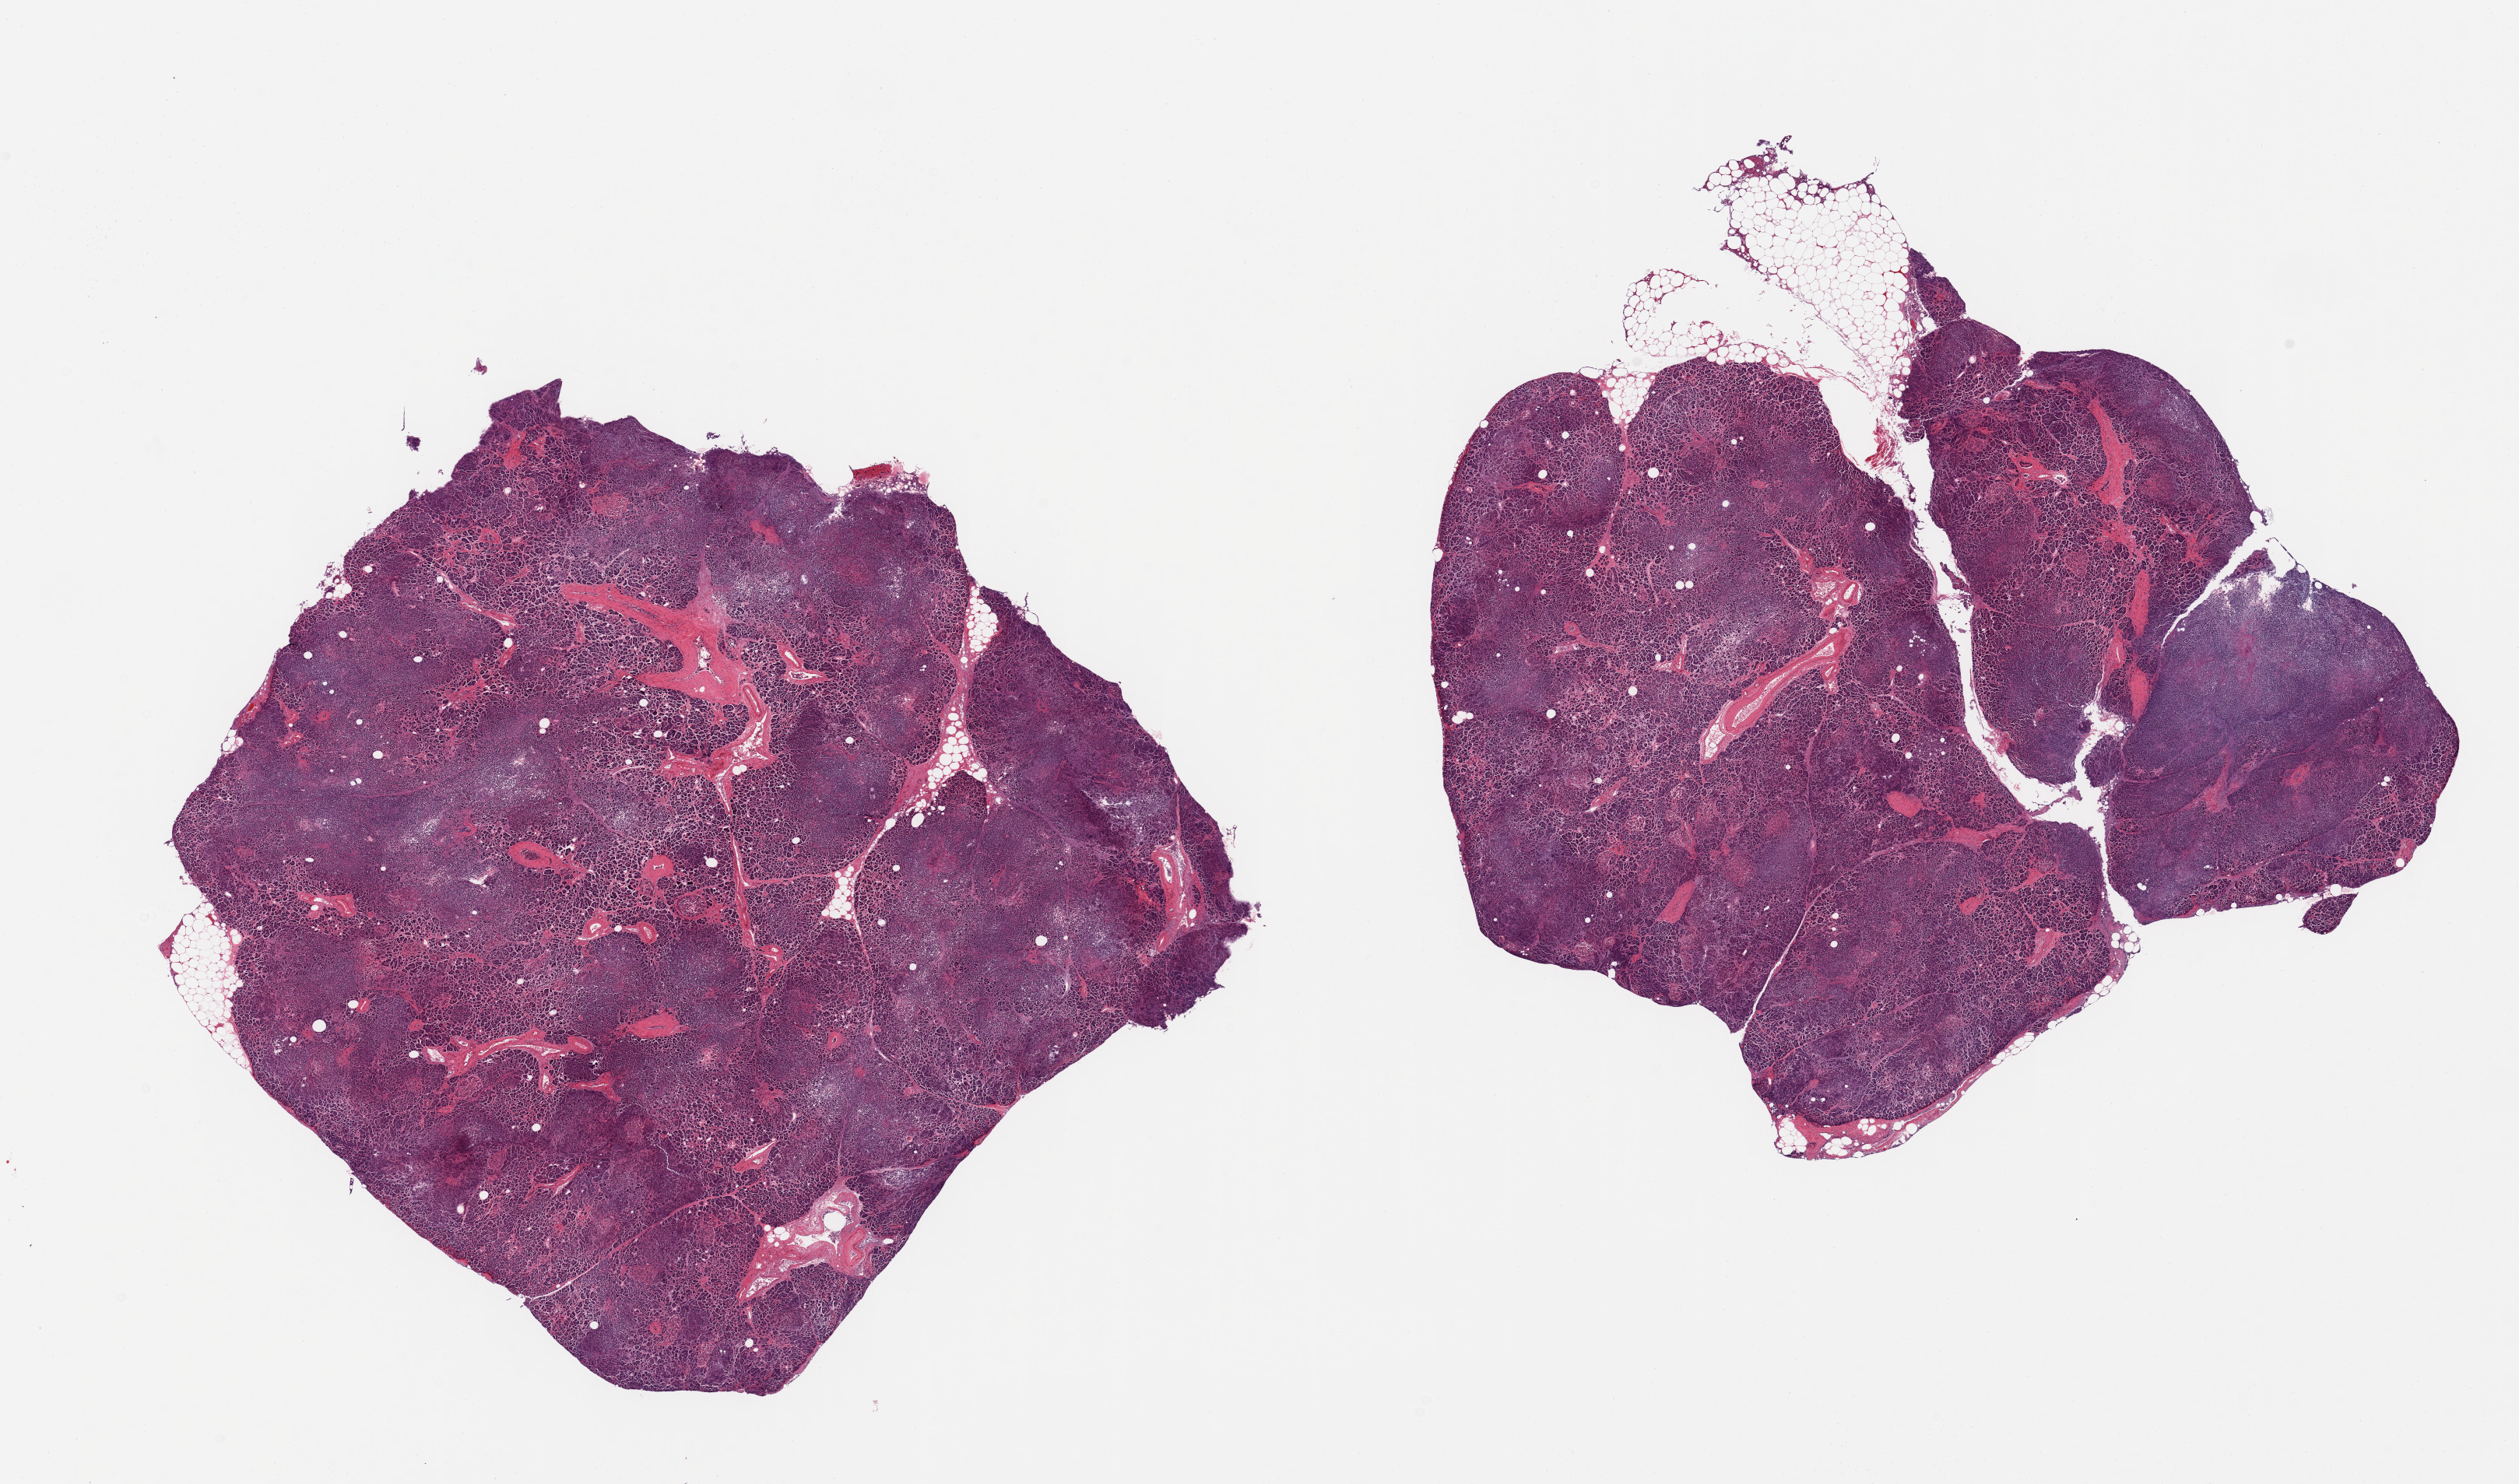
H&E whole-slide image, shown as a low-resolution overview of the whole scanned area (about 25.6 x 15.1 mm). PAXgene-fixed paraffin-embedded (PFPE) section. Sampled site (target tissue): pancreas. Donor tissue sample. Donor sex: male.
Pathologist's review note for this sample: 2 pieces; 1 includes ~10% attached fat, moderate to severe autolysis.